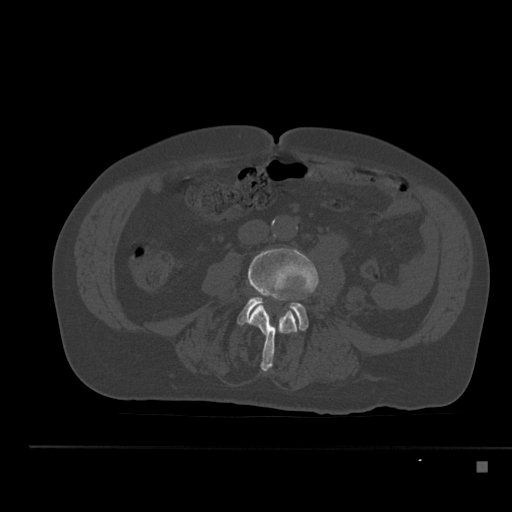
CT including the spine, one axial slice. Slice 155 of 517 in the series (ordered by position). Reconstruction kernel Br40s. 120 kVp. Bone window (W 1800 / L 400 HU). 1.5 mm slice thickness. 512 × 512 image matrix, field of view 408 × 408 mm. Male patient, age 70 years. From the clinical record (not read from this slice): primary cancer: renal; vertebrae with lytic lesions (as recorded): T4, T6, T10, T12, L3, L4, L5.
Annotated regions visible in this slice (semi-automatic segmentation, software-assisted and operator-edited):
- L3 vertebra: bounding box (x1, y1, x2, y2) in pixels: (248, 248, 319, 372)
- L4 vertebra: (238, 298, 309, 330)